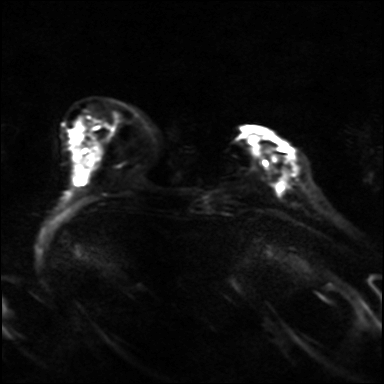
Breast MRI, one axial slice; slice 6 of 36 in the series (ordered by position); diffusion-weighted series; image 2 of 4 stored at this slice position (different b-values; order by instance number); 3 T; 4 mm slice thickness; 384 × 384 image matrix, field of view 320 × 320 mm. Female patient.
Annotated regions visible in this slice (outlined manually by an expert reader):
- tumour on diffusion-weighted imaging: box from (x=284, y=160) to (x=291, y=182) px